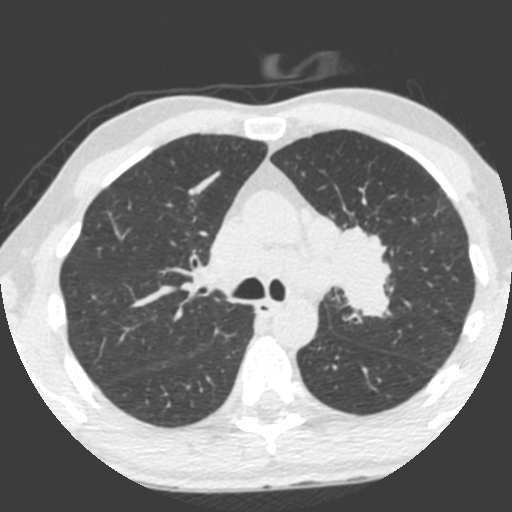
Low-dose screening chest CT, axial slice. Third annual screen. Lung window (W 1500 / L -600 HU). Slice 145 of 212 in the series. Male, age 55 years at enrolment. Current smoker at enrolment.
• Lesion marked by an expert reader, bounding box <309,226,393,323> (left, top, right, bottom; pixels).
• Reader record for this screening exam (exam-level; its link to the box is not recorded): non-calcified nodule or mass ≥4 mm, left upper lobe, 49 × 29 mm, spiculated (stellate) margins, soft tissue attenuation, pre-existing on the prior screen: yes; interval growth: yes.
• Official screen result: positive, other.